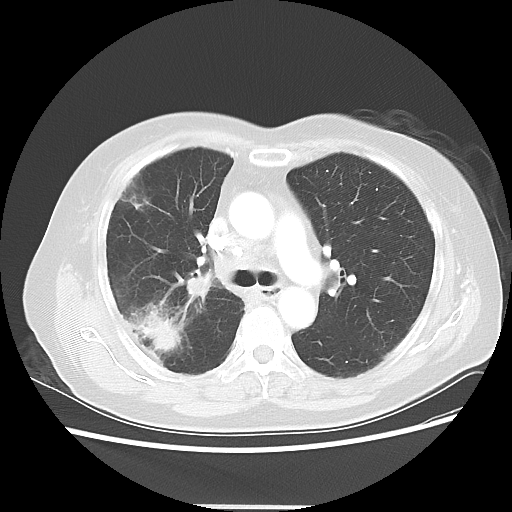
Chest CT, one axial slice; slice 31 of 50 in the series (ordered by position); reconstruction kernel LUNG; 120 kVp; lung window (W 1500 / L -600 HU); 5 mm slice thickness; 512 × 512 image matrix. Female patient, age 72 years. From the clinical record (not read from this slice): clinical TNM (as recorded): T2 N1 M0; histopathological grade: G1.
Annotated regions visible in this slice (bounding box drawn by a radiologist):
- lung tumour (recorded histology: adenocarcinoma): bounding box <126,300,185,357> (left, top, right, bottom; pixels)